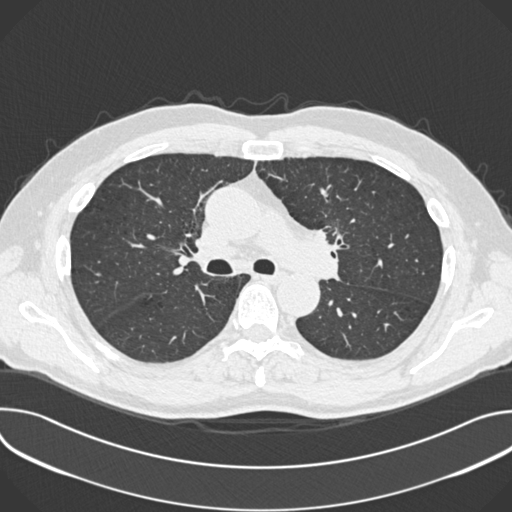
Low-dose screening chest CT, one axial slice. Position 239 of 361 along the scan axis. 120 kVp. Lung window (W 1500 / L -600 HU). 1 mm slice thickness. 512 × 512 image matrix.
Annotated regions visible in this slice (outlined manually by an expert reader):
- lesion 1 (tumor, upper lobe of left lung): box from (x=316, y=230) to (x=342, y=248) px